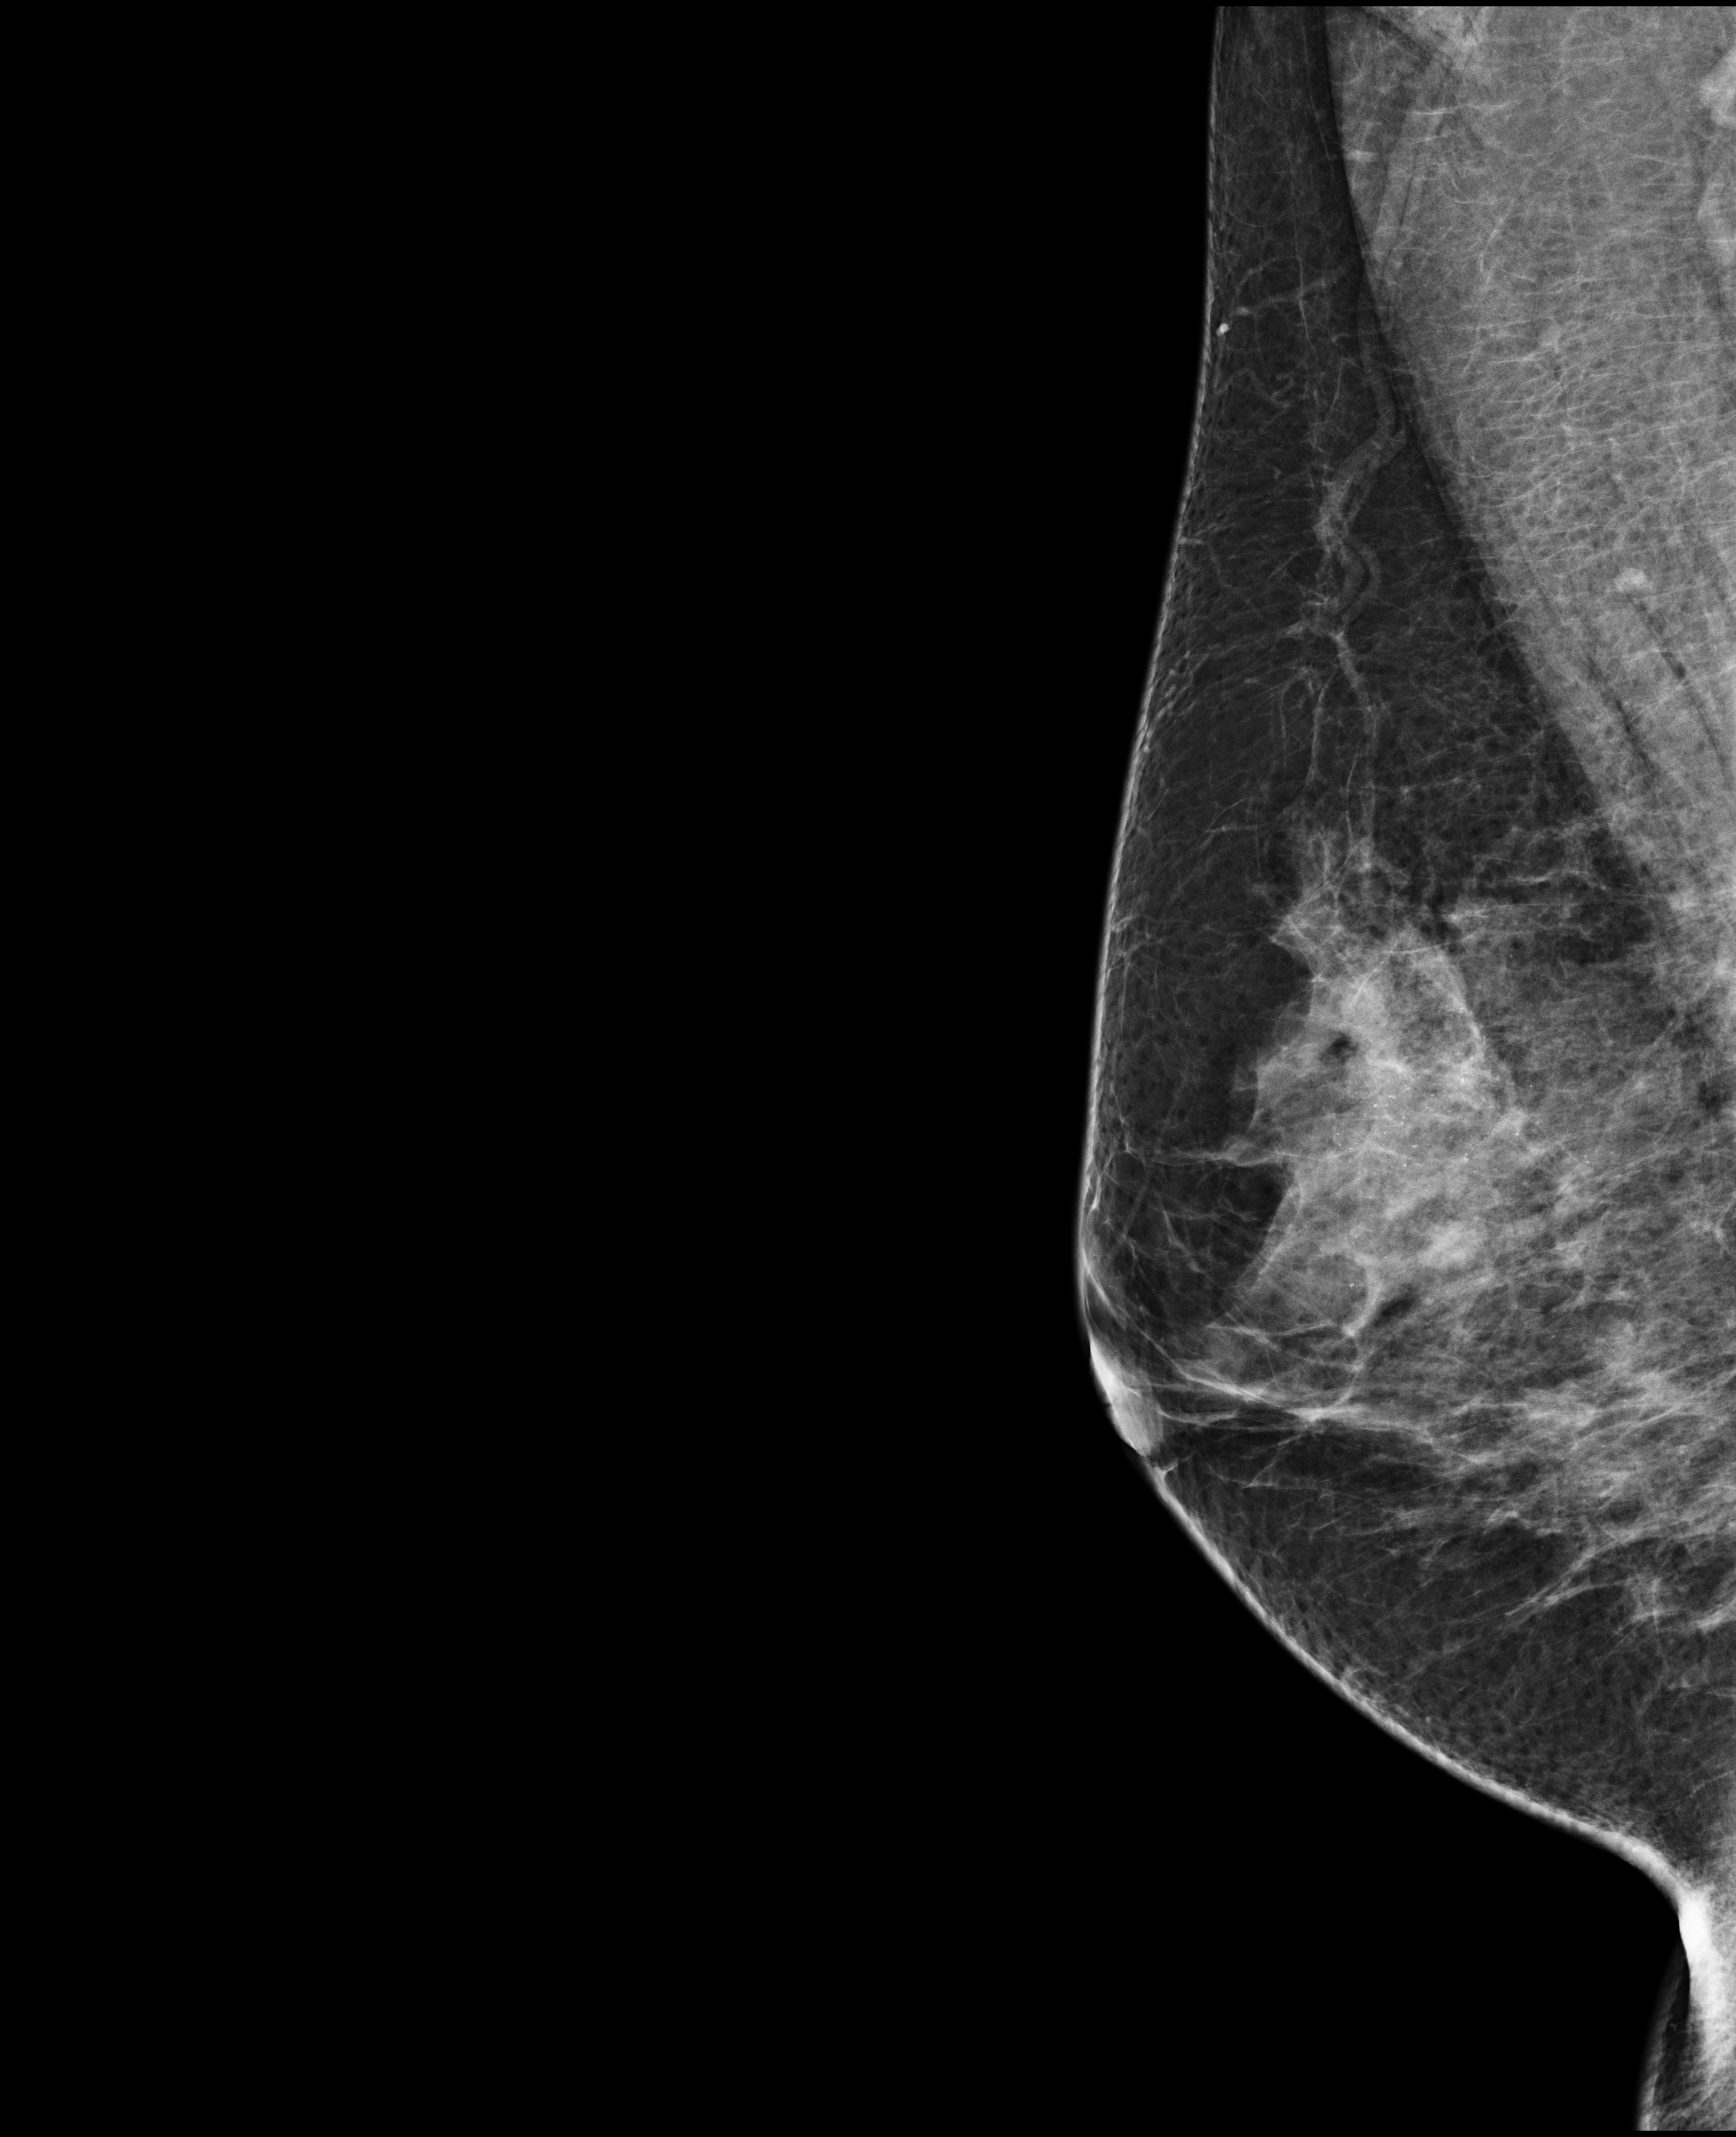
Annual screening mammography examination; compressed breast thickness 57 mm. Patient aged 48 years (female).
Image type: full-field digital mammogram. Breast: right. Projection: MLO view.